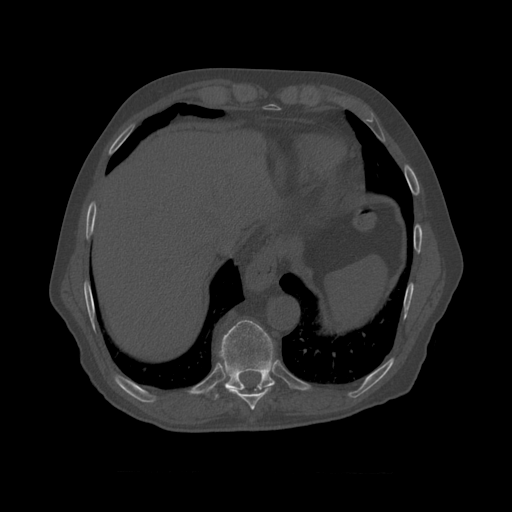
CT including the spine, one axial slice; position 435 of 450 along the scan axis; reconstruction kernel STANDARD; bone window (W 1800 / L 400 HU); 512 × 512 image matrix. Patient age 75 years. Case-level facts recorded for this patient, not image findings: primary cancer: prostate.
Outlined on this slice (semi-automatically segmented with operator editing):
- T8 vertebra: box from (x=222, y=342) to (x=274, y=410) px
- T9 vertebra: (x=215, y=320)–(x=275, y=392)